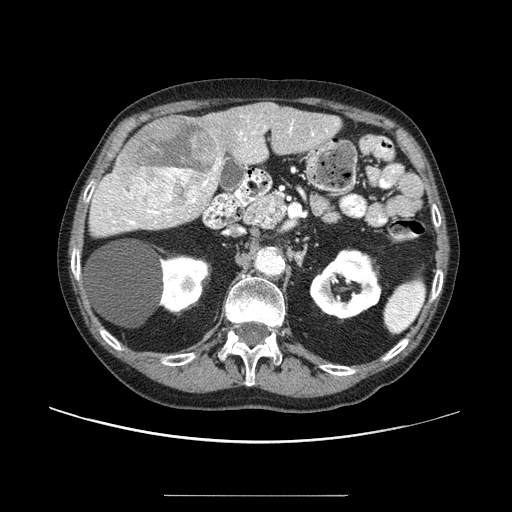
Contrast-enhanced abdominal CT (liver protocol), one axial slice; slice 45 of 91 in the series (ordered by position); reconstruction kernel STANDARD; one of 2 acquisitions stored at this slice position; soft-tissue window (W 400 / L 40 HU); 2.5 mm slice thickness; 512 × 512 image matrix, field of view 400 × 400 mm. Case-level facts recorded for this patient, not image findings: diagnosis: hepatocellular carcinoma (patient treated with transarterial chemoembolisation; whether this scan precedes or follows treatment is not stated here); TNM stage (as recorded): Stage-I; Child-Pugh class: A; tumour nodularity: uninodular.
Outlined on this slice (semi-automatically segmented with operator editing):
- liver parenchyma outside the tumour (the mass and vessels are separate outlines, so this box may not span the whole liver): bounding box <90,102,340,236> (left, top, right, bottom; pixels)
- mass: <114,114,220,214>
- liver vessels: <106,124,314,225>